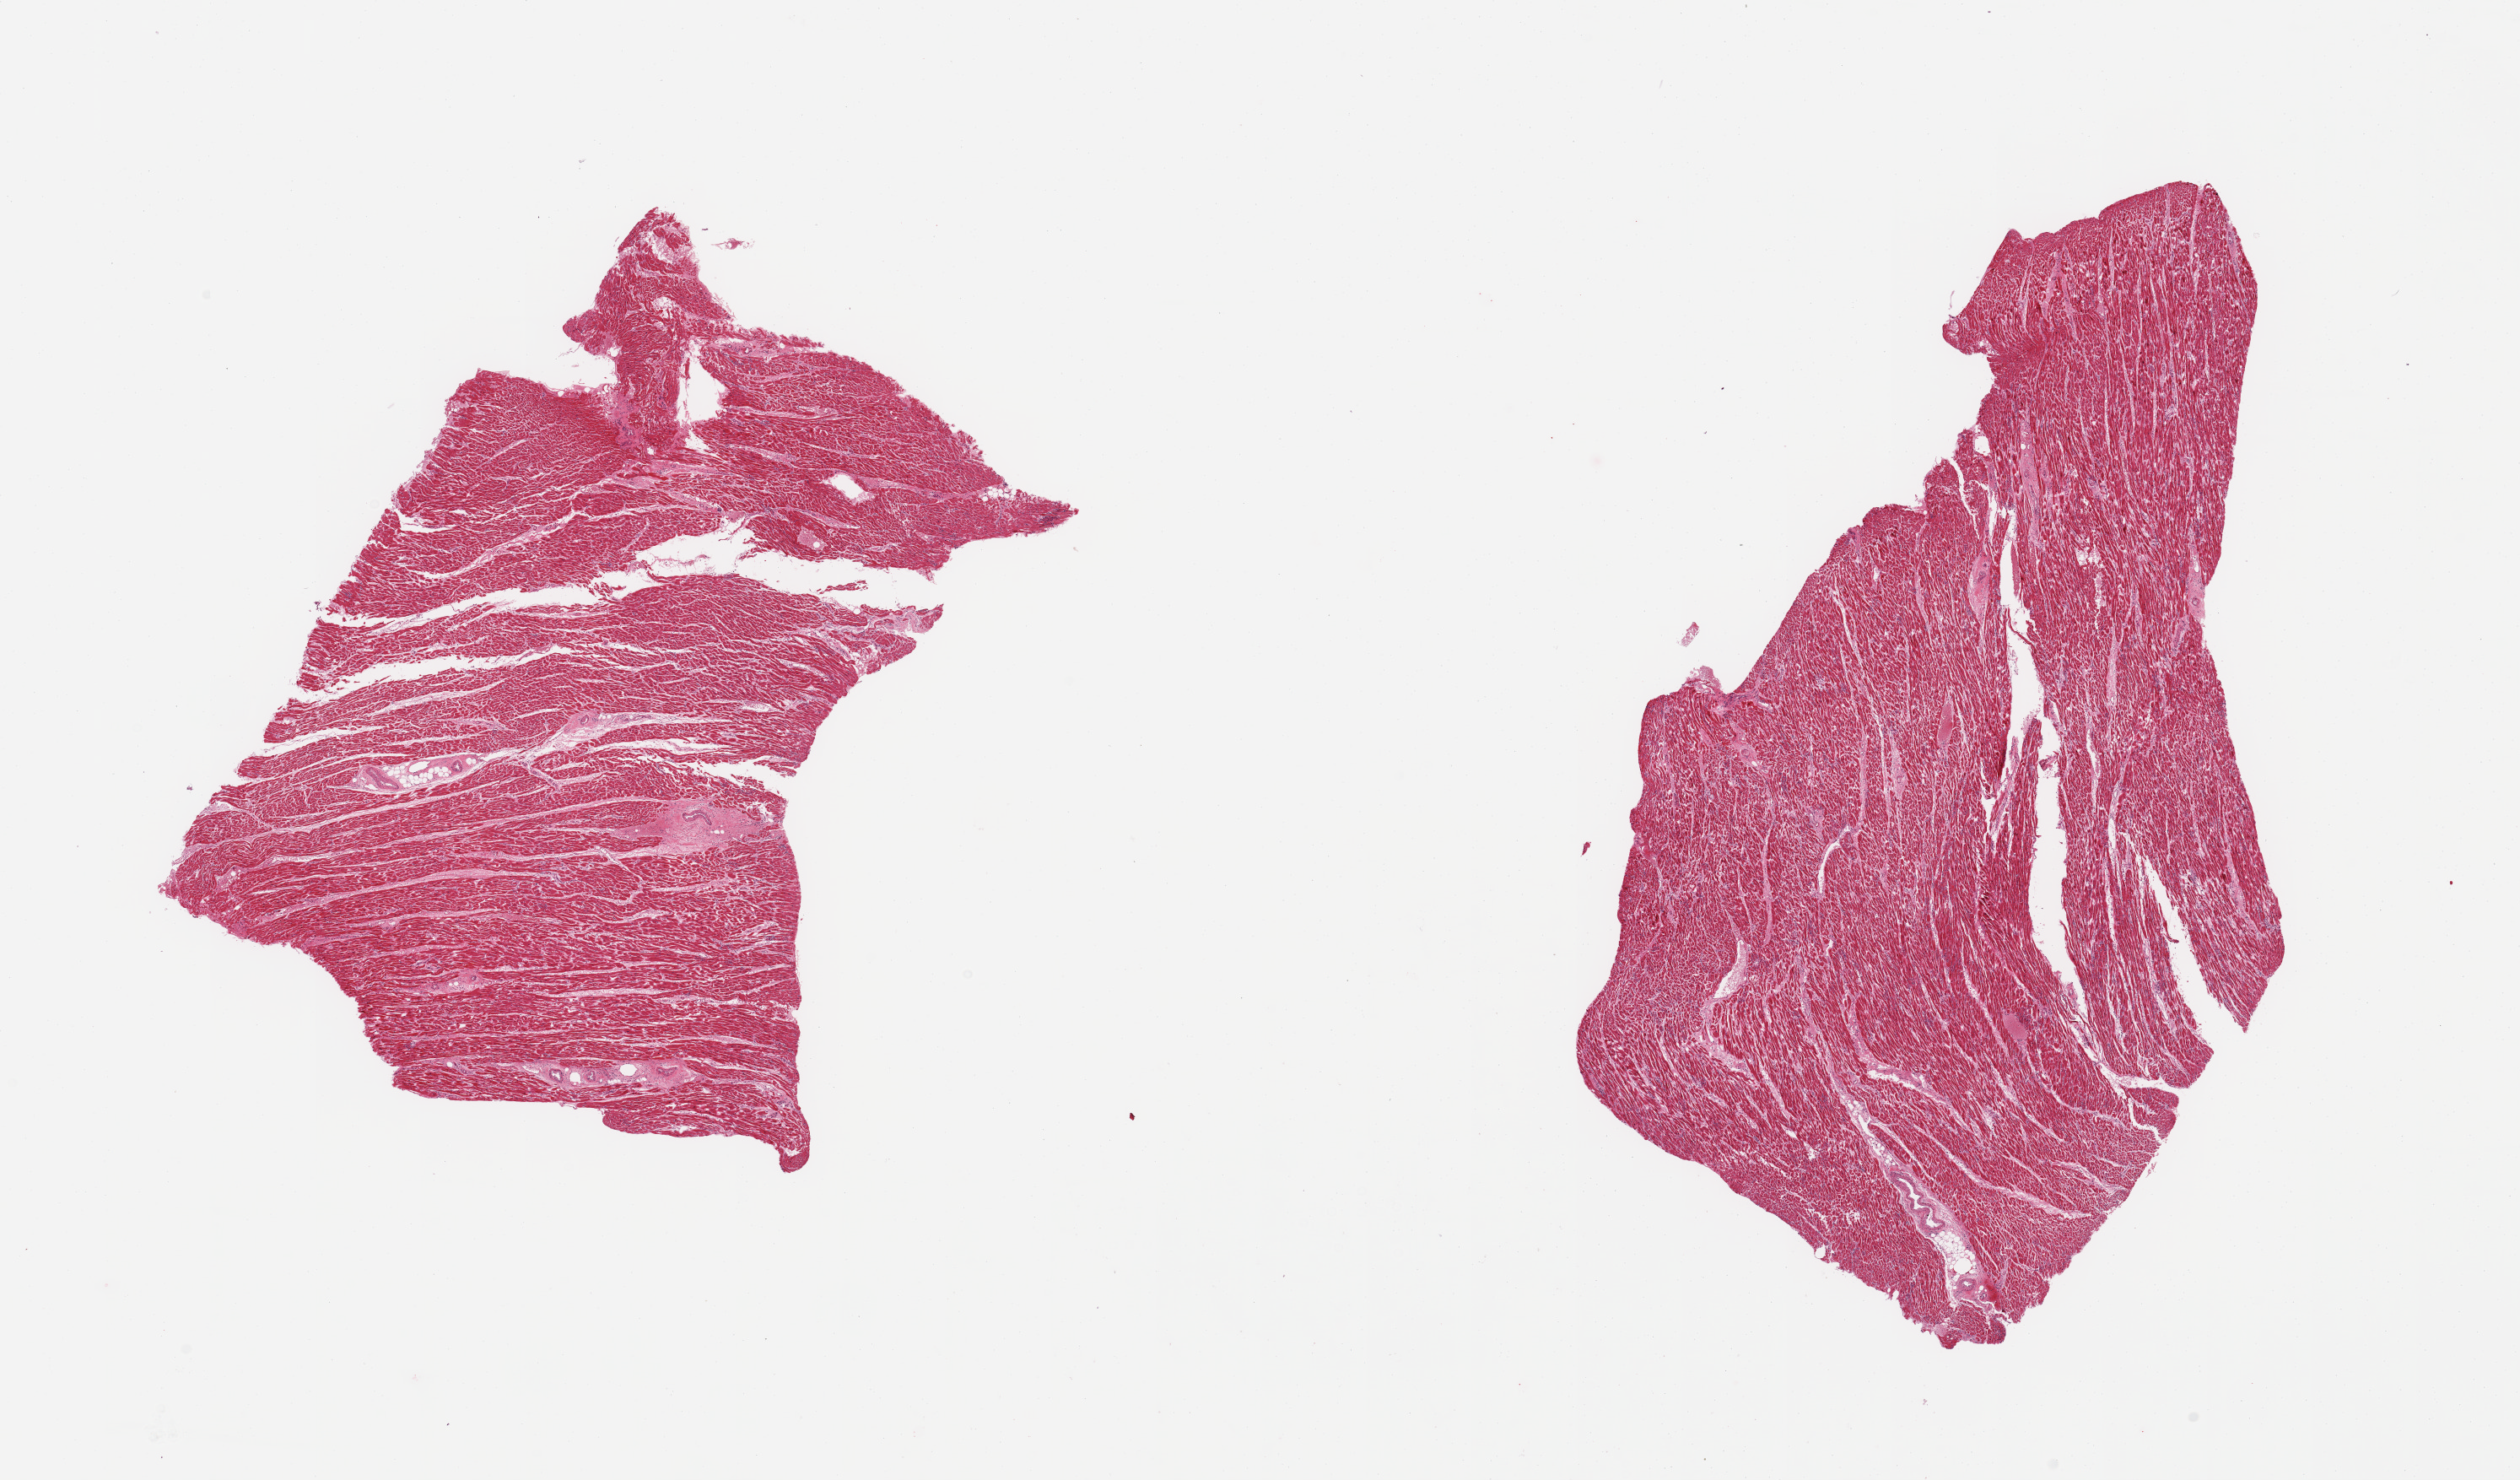
Digitized haematoxylin and eosin-stained section — whole scanned area (about 23.6 x 13.9 mm, acquisition: 20x scan) shown as a low-resolution overview. PAXgene-fixed, paraffin-embedded tissue. Section of heart (target tissue). Tissue donor sample.
* review note (as recorded): 2 pieces, patchy mild/moderate myocarditis, lymphocytic, with myocyte destruction